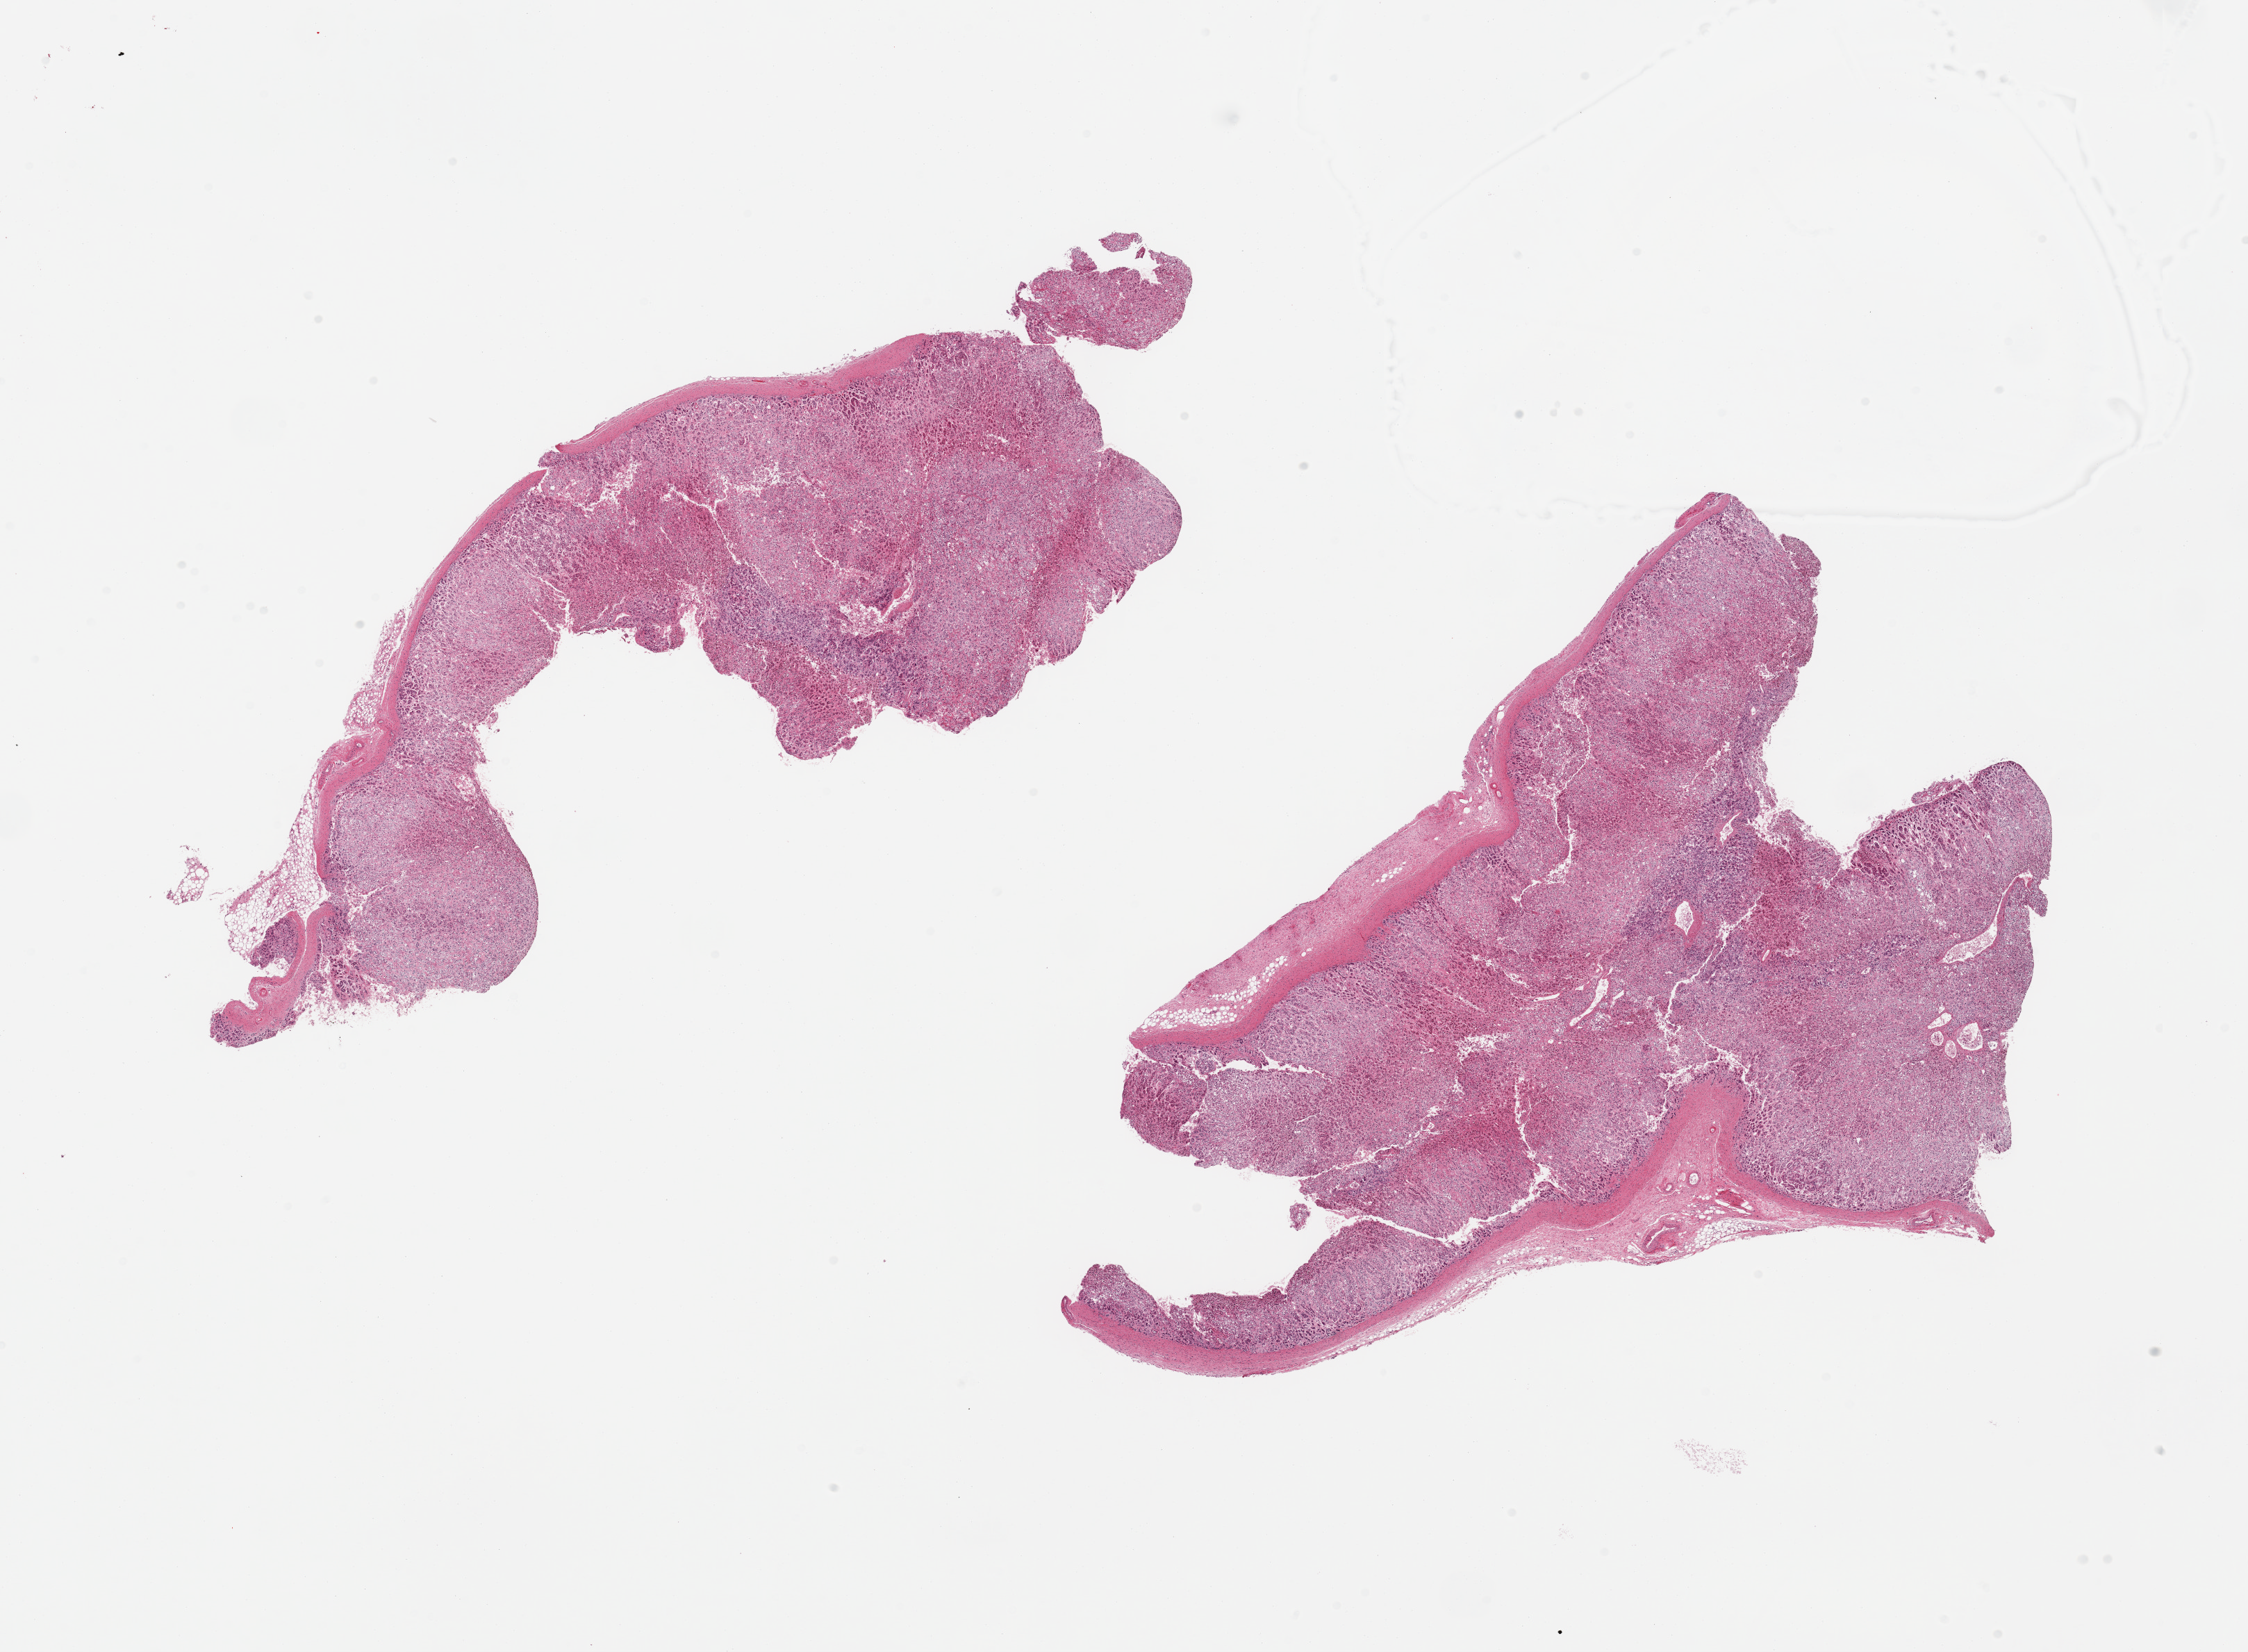
Whole-slide image, hematoxylin and eosin (H&E) stain, brightfield — shown as a low-resolution overview of the whole scanned area (about 25.6 x 18.8 mm, slide scanned at 20x); PAXgene-fixed paraffin-embedded (PFPE) section; section of adrenal gland (target tissue); donor tissue sample.
* pathologist's review note for this sample: 2 pieces, cortex, advanced autolysis